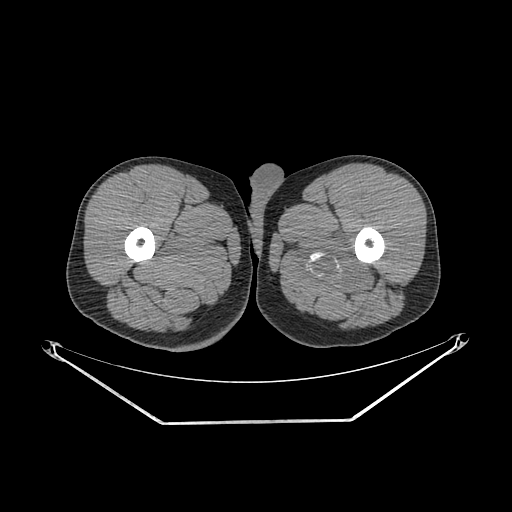
CT of an extremity soft-tissue mass (from a PET/CT study), one axial slice; position 252 of 267 along the scan axis; reconstruction kernel SOFT; soft-tissue window (W 400 / L 40 HU); 3.75 mm slice thickness; 512 × 512 image matrix, field of view 500 × 500 mm. Male patient. From the clinical record (not read from this slice): histological type: extraskeletal osteosarcoma; grade: high; site of the primary tumour: left adductur.
Outlined on this slice (expert contour drawn on MRI and transferred to this co-registered scan by the dataset authors):
- gross tumour volume (mass): box from (x=290, y=224) to (x=378, y=298) px